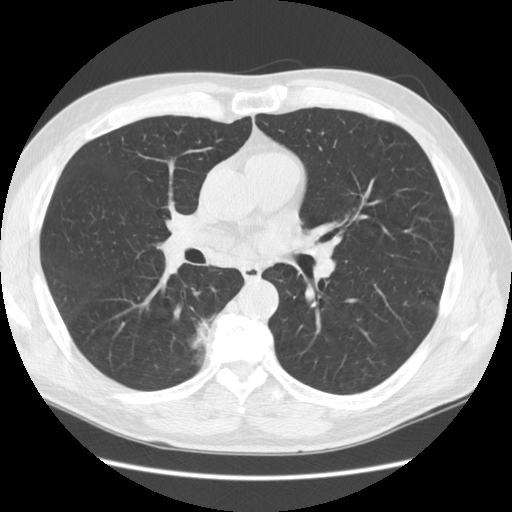
Chest CT (low-dose screening protocol), one axial image; second screening round (one year after baseline); lung window (W 1500 / L -600 HU); 2.5 mm slice thickness; slice 62 of 133 in the series. Male, age 69 years at enrolment.
Expert-annotated lung lesion, bounding box <169,306,231,366> (left, top, right, bottom; pixels). The screening reader recorded 2 non-calcified nodules or masses ≥4 mm on this exam; which of them this box marks is not recorded. Official screen result: positive, other. Lung cancer was diagnosed 88 days after this screen: bronchiolo-alveolar adenocarcinoma, NOS, right lower lobe, well differentiated (G1), stage IB (AJCC 6th edition), 23 mm at pathology.